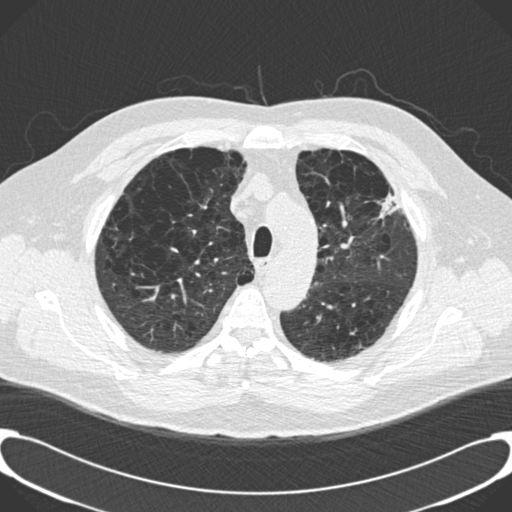
Low-dose screening chest CT, axial slice; third screening round (two years after baseline); lung window (W 1500 / L -600 HU); 2 mm slice thickness; standard (soft-tissue) reconstruction kernel (B30f); slice 39 of 189 in the series; 512 × 512 image matrix, field of view 380 × 380 mm. Male, age 59 years at enrolment. Current smoker at enrolment.
Expert reader's lesion annotation, bounding box <361,168,412,227> (left, top, right, bottom; pixels). Screening reader's record for this exam: no non-calcified nodule ≥4 mm recorded.